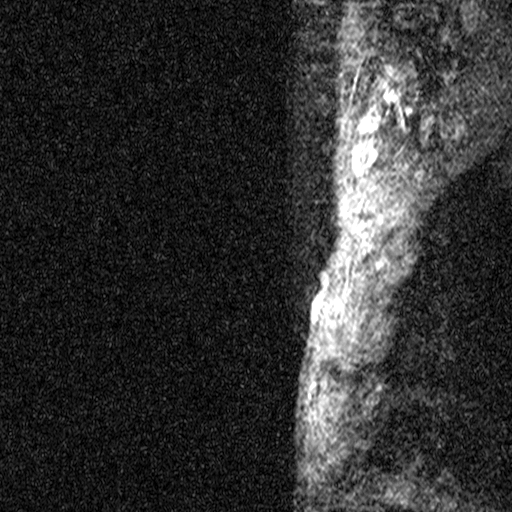
Breast MRI (dynamic contrast-enhanced), one sagittal slice. Position 39 of 44 along the scan axis. Dynamic contrast-enhanced study with each time point stored as its own series, time point 2 of 3 at this slice position (early post-contrast, ordered by acquisition time). 1.5 T. TE 4.5 ms, TR 11 ms. 3 mm slice thickness. 512 × 512 image matrix. Patient: female, 45 years. From the clinical record (not read from this slice): setting: breast cancer imaged before/during neoadjuvant chemotherapy; receptor status: HR-positive, HER2-negative.
Annotated regions visible in this slice (semi-automatically segmented with operator editing):
- analysis volume of interest (the breast-tissue region the enhancement analysis was run in; not a lesion): box from (x=256, y=218) to (x=351, y=359) px
- tumour enhancement mask (voxels above the 90 % enhancement threshold inside the analysis volume of interest): (x=311, y=304)–(x=313, y=306)